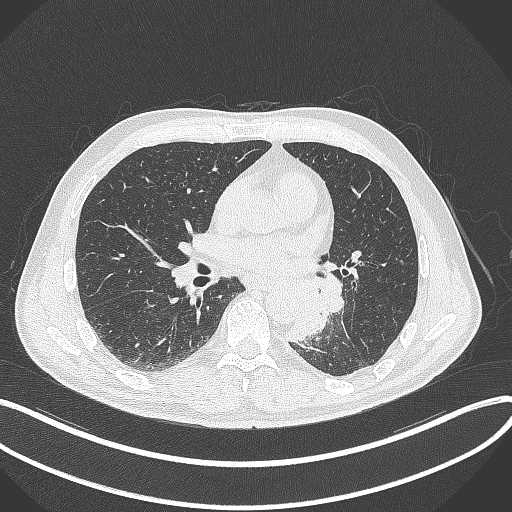
Chest CT, one axial slice; position 162 of 329 along the scan axis; lung window (W 1500 / L -600 HU); 512 × 512 image matrix. Patient: male, 59 years. From the clinical record (not read from this slice): clinical TNM (as recorded): T2a N2 M0.
Annotated regions visible in this slice (rectangle marked by the reading radiologist):
- lung tumour (recorded histology: squamous cell carcinoma): box from (x=287, y=273) to (x=349, y=342) px